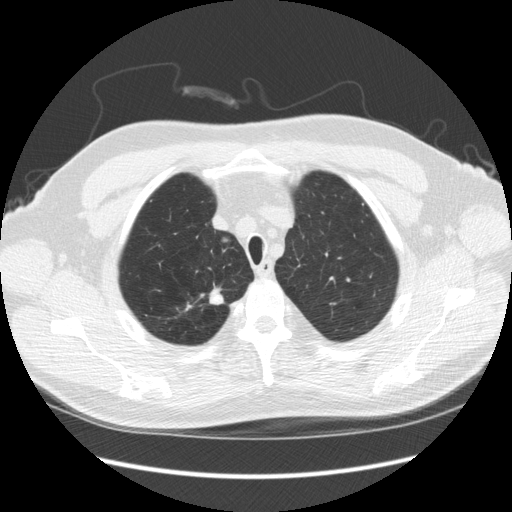
Chest CT (low-dose screening protocol), one axial image; third screening round (two years after baseline); lung window (W 1500 / L -600 HU); 2.5 mm slice thickness; standard (soft-tissue) reconstruction kernel (STANDARD); 120 kVp; slice 34 of 248 in the series. Male, age 64 years at enrolment. Former smoker at enrolment.
2 lesions marked by an expert reader on this slice (largest first), box from (x=201, y=230) to (x=243, y=259) px; (x=197, y=282)–(x=231, y=315). The screening reader recorded 4 non-calcified nodules or masses ≥4 mm on this exam (right upper lobe, right upper lobe, right upper lobe, right upper lobe); which of them these boxes mark is not recorded. Official screen result: positive, other.